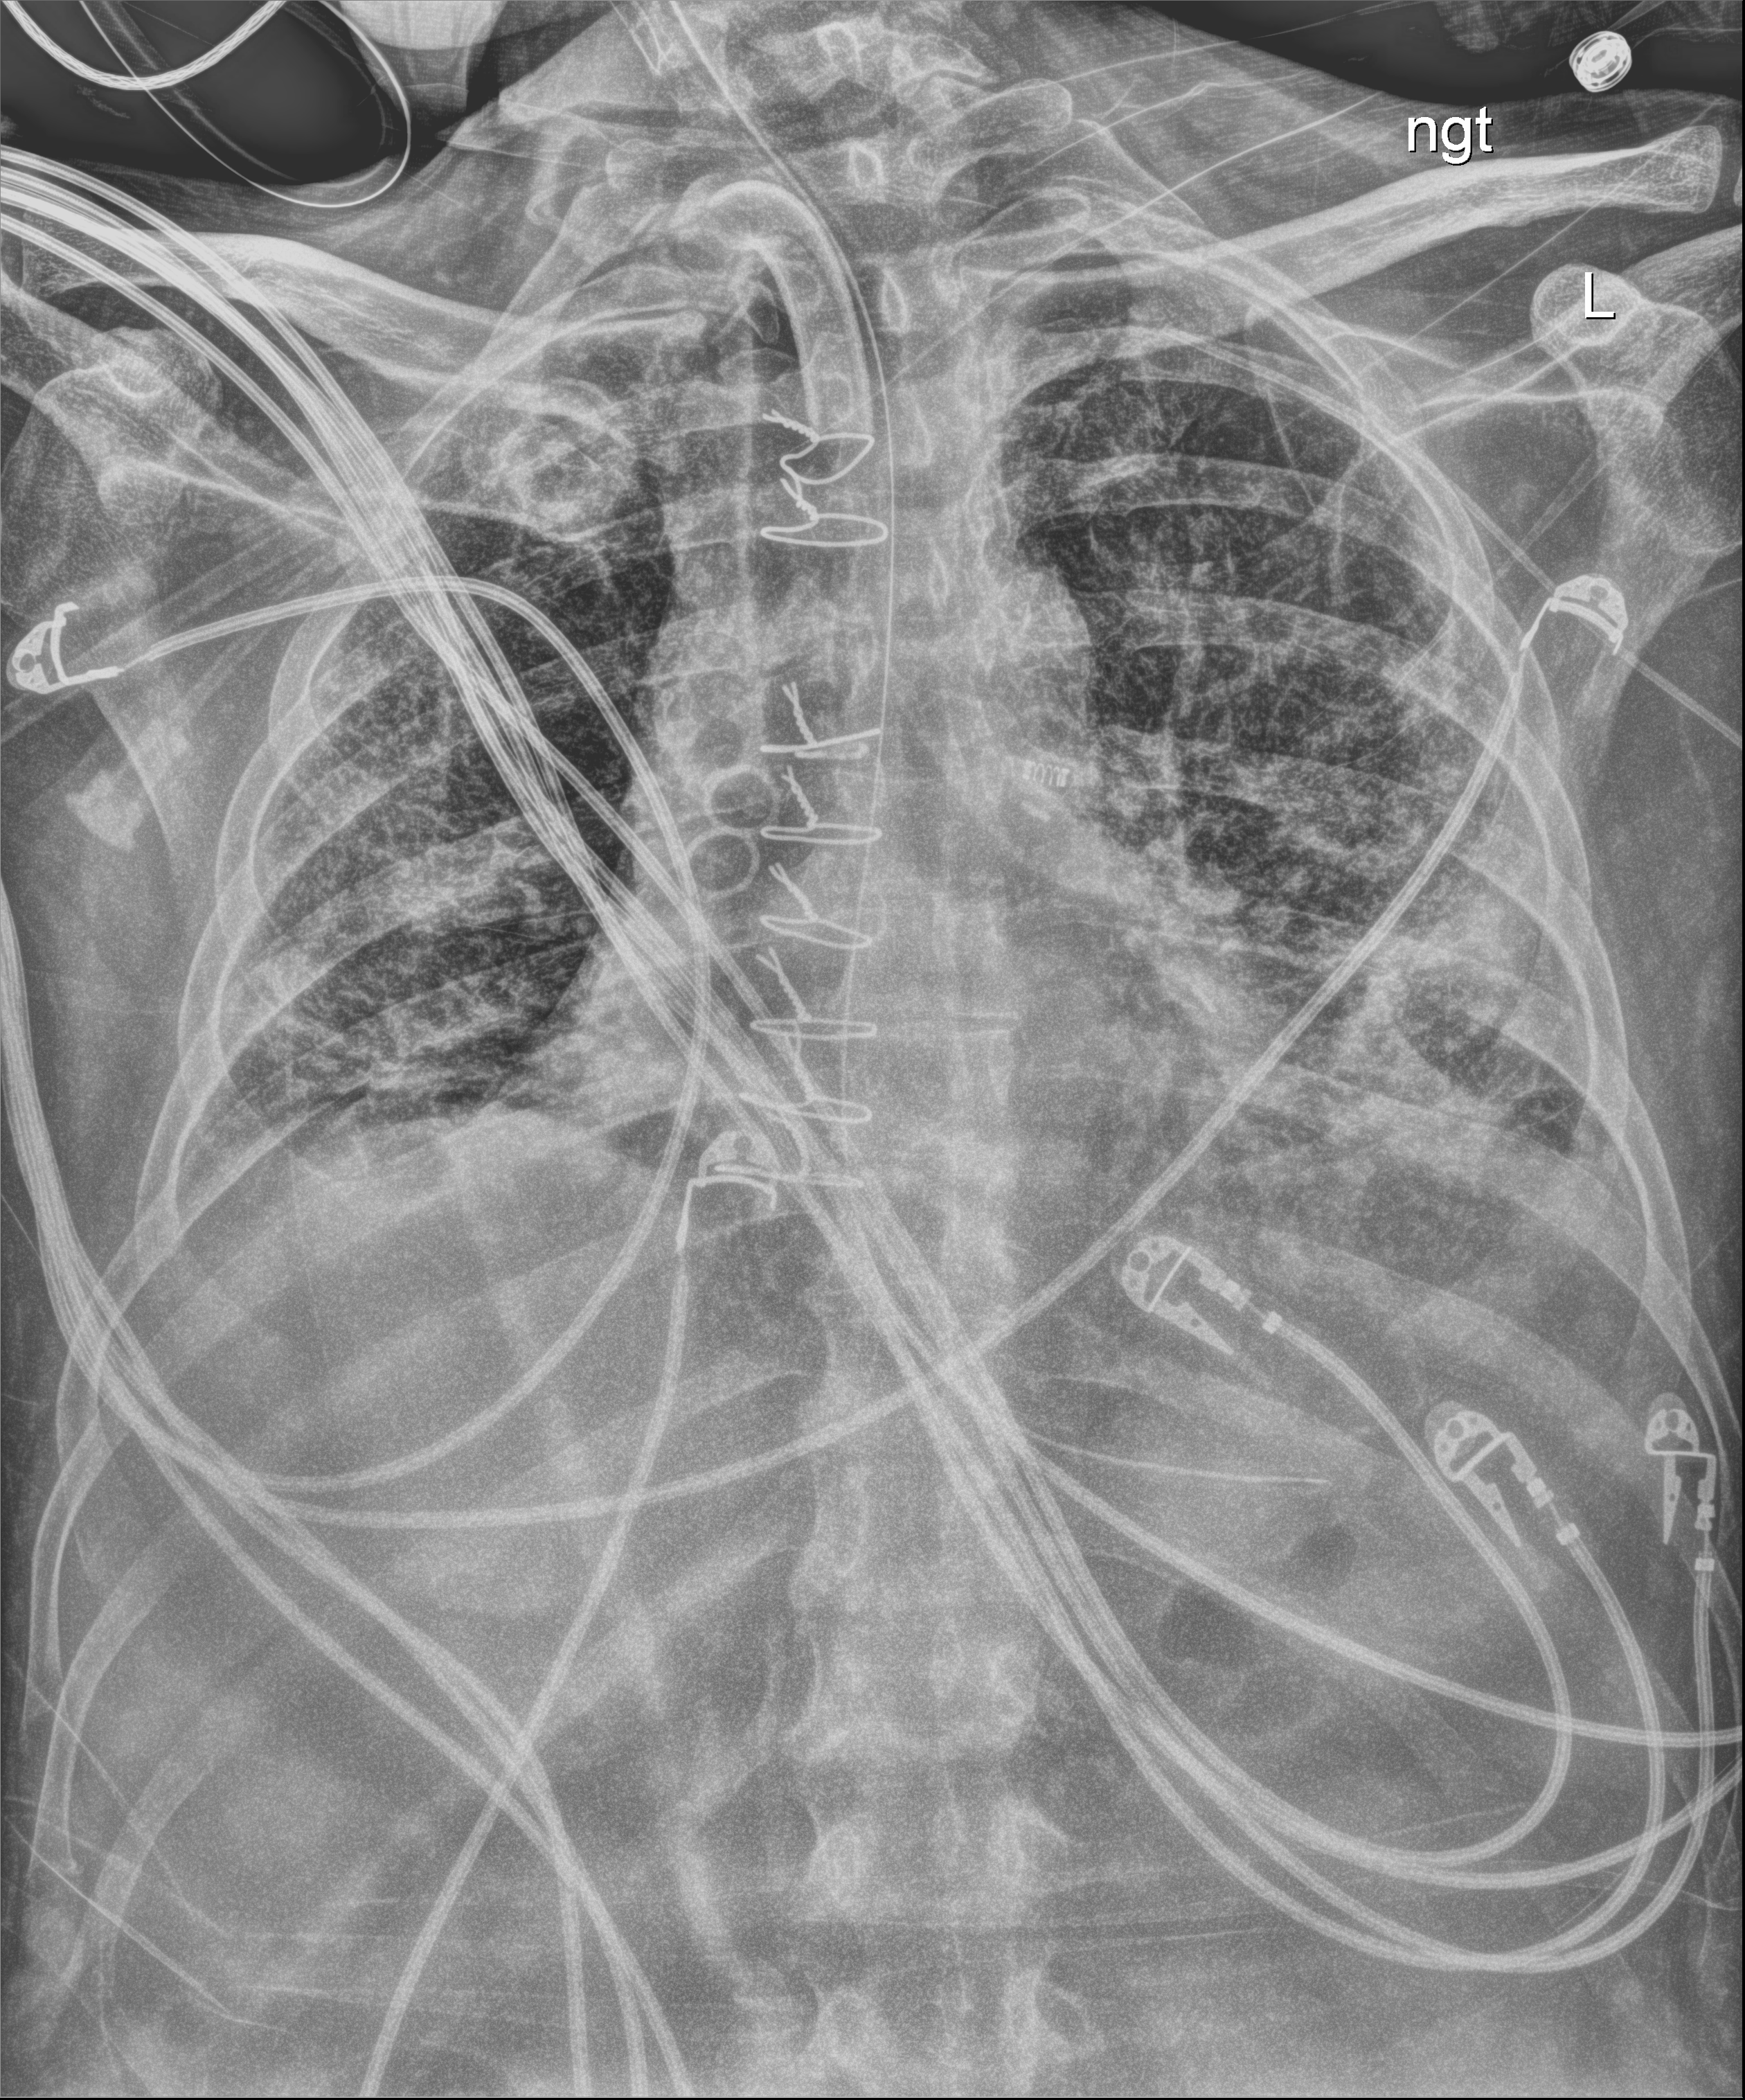
Chest X-ray; anteroposterior (AP) projection. Patient hospitalised with COVID-19; male, aged 18–59 years.
From the hospital-stay record, not from the radiograph (when in the stay this image was taken is not recorded): other chronic lung disease (admission record): yes; mechanically ventilated during this hospital stay: yes; admitted to intensive care during this hospital stay: yes.